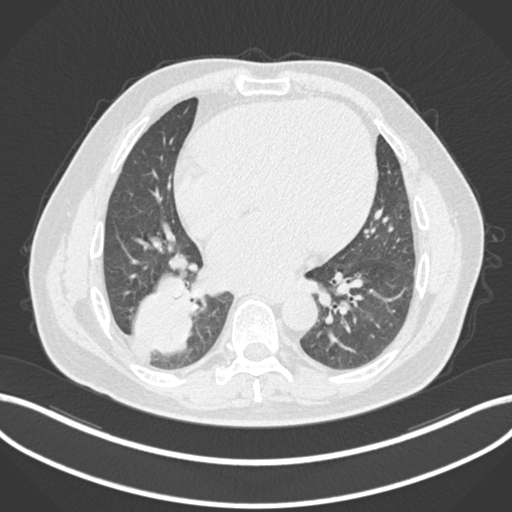
Chest CT, one axial slice. Reconstruction kernel B30f. 120 kVp. Lung window (W 1500 / L -600 HU). 512 × 512 image matrix, field of view 400 × 400 mm. Male patient, age 59 years.
Outlined on this slice (bounding box drawn by a radiologist):
- lung tumour (recorded histology: adenocarcinoma): bounding box <131,268,194,357> (left, top, right, bottom; pixels)